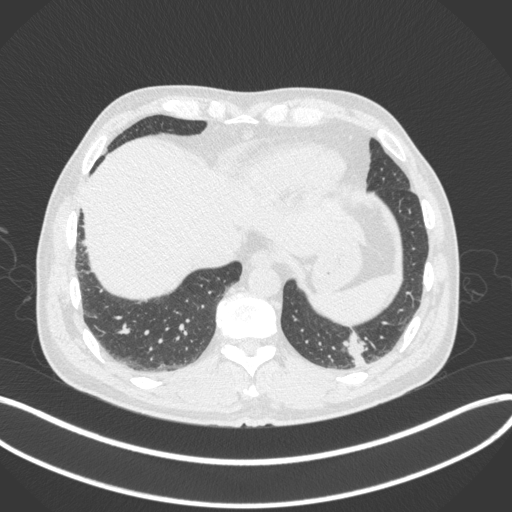
Chest CT, one axial slice. Slice 55 of 313 in the series (ordered by position). Reconstruction kernel B31f. 120 kVp. Lung window (W 1500 / L -600 HU). 1 mm slice thickness. 512 × 512 image matrix, field of view 400 × 400 mm. Patient: male, 54 years. From the clinical record (not read from this slice): clinical TNM (as recorded): T1c N0 M1; histopathological grade: G3.
Outlined on this slice (bounding box drawn by a radiologist):
- lung tumour (recorded histology: adenocarcinoma): box from (x=340, y=325) to (x=371, y=369) px